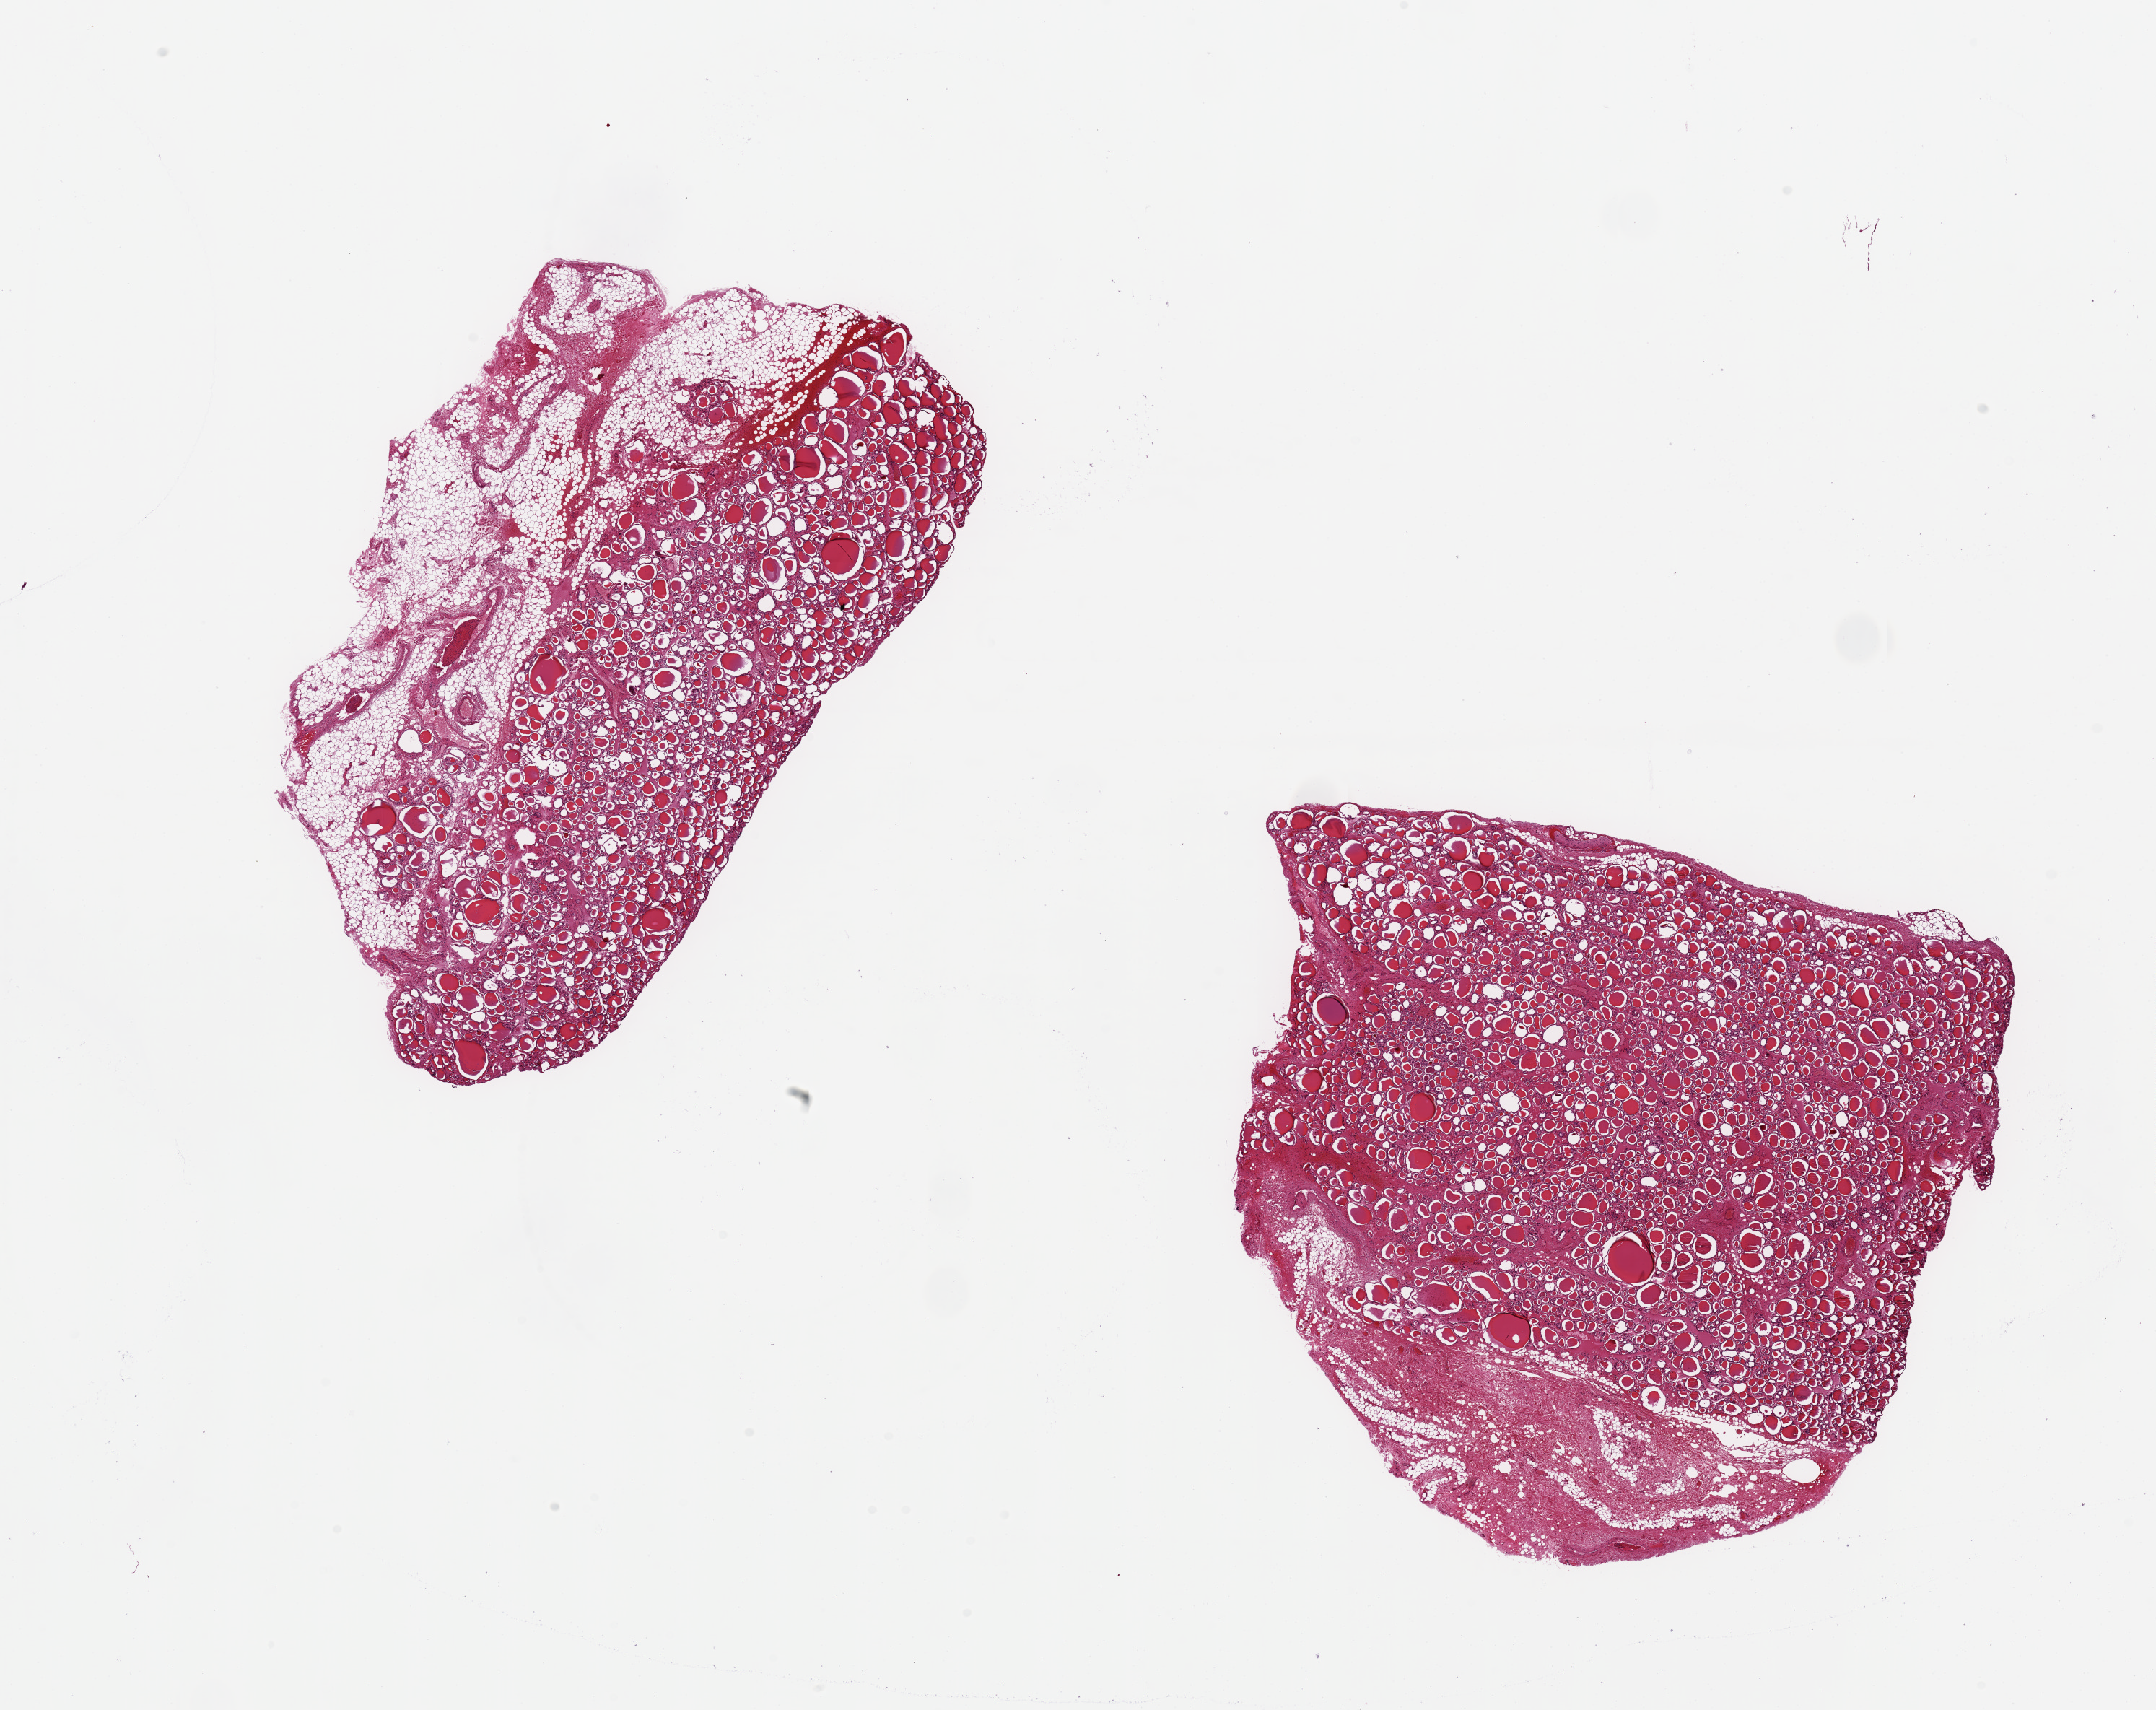
Whole-slide image, H&E stain, shown as a low-resolution overview of the whole scanned area (about 23.6 x 18.7 mm, from a 20x scan), PAXgene-fixed paraffin-embedded (PFPE) section, section of thyroid (target tissue), donor tissue sample. Donor: male.
• pathologist's review note for this sample: 2 pieces, ~ 8x6mm. One ~ 25% adipose on one edge